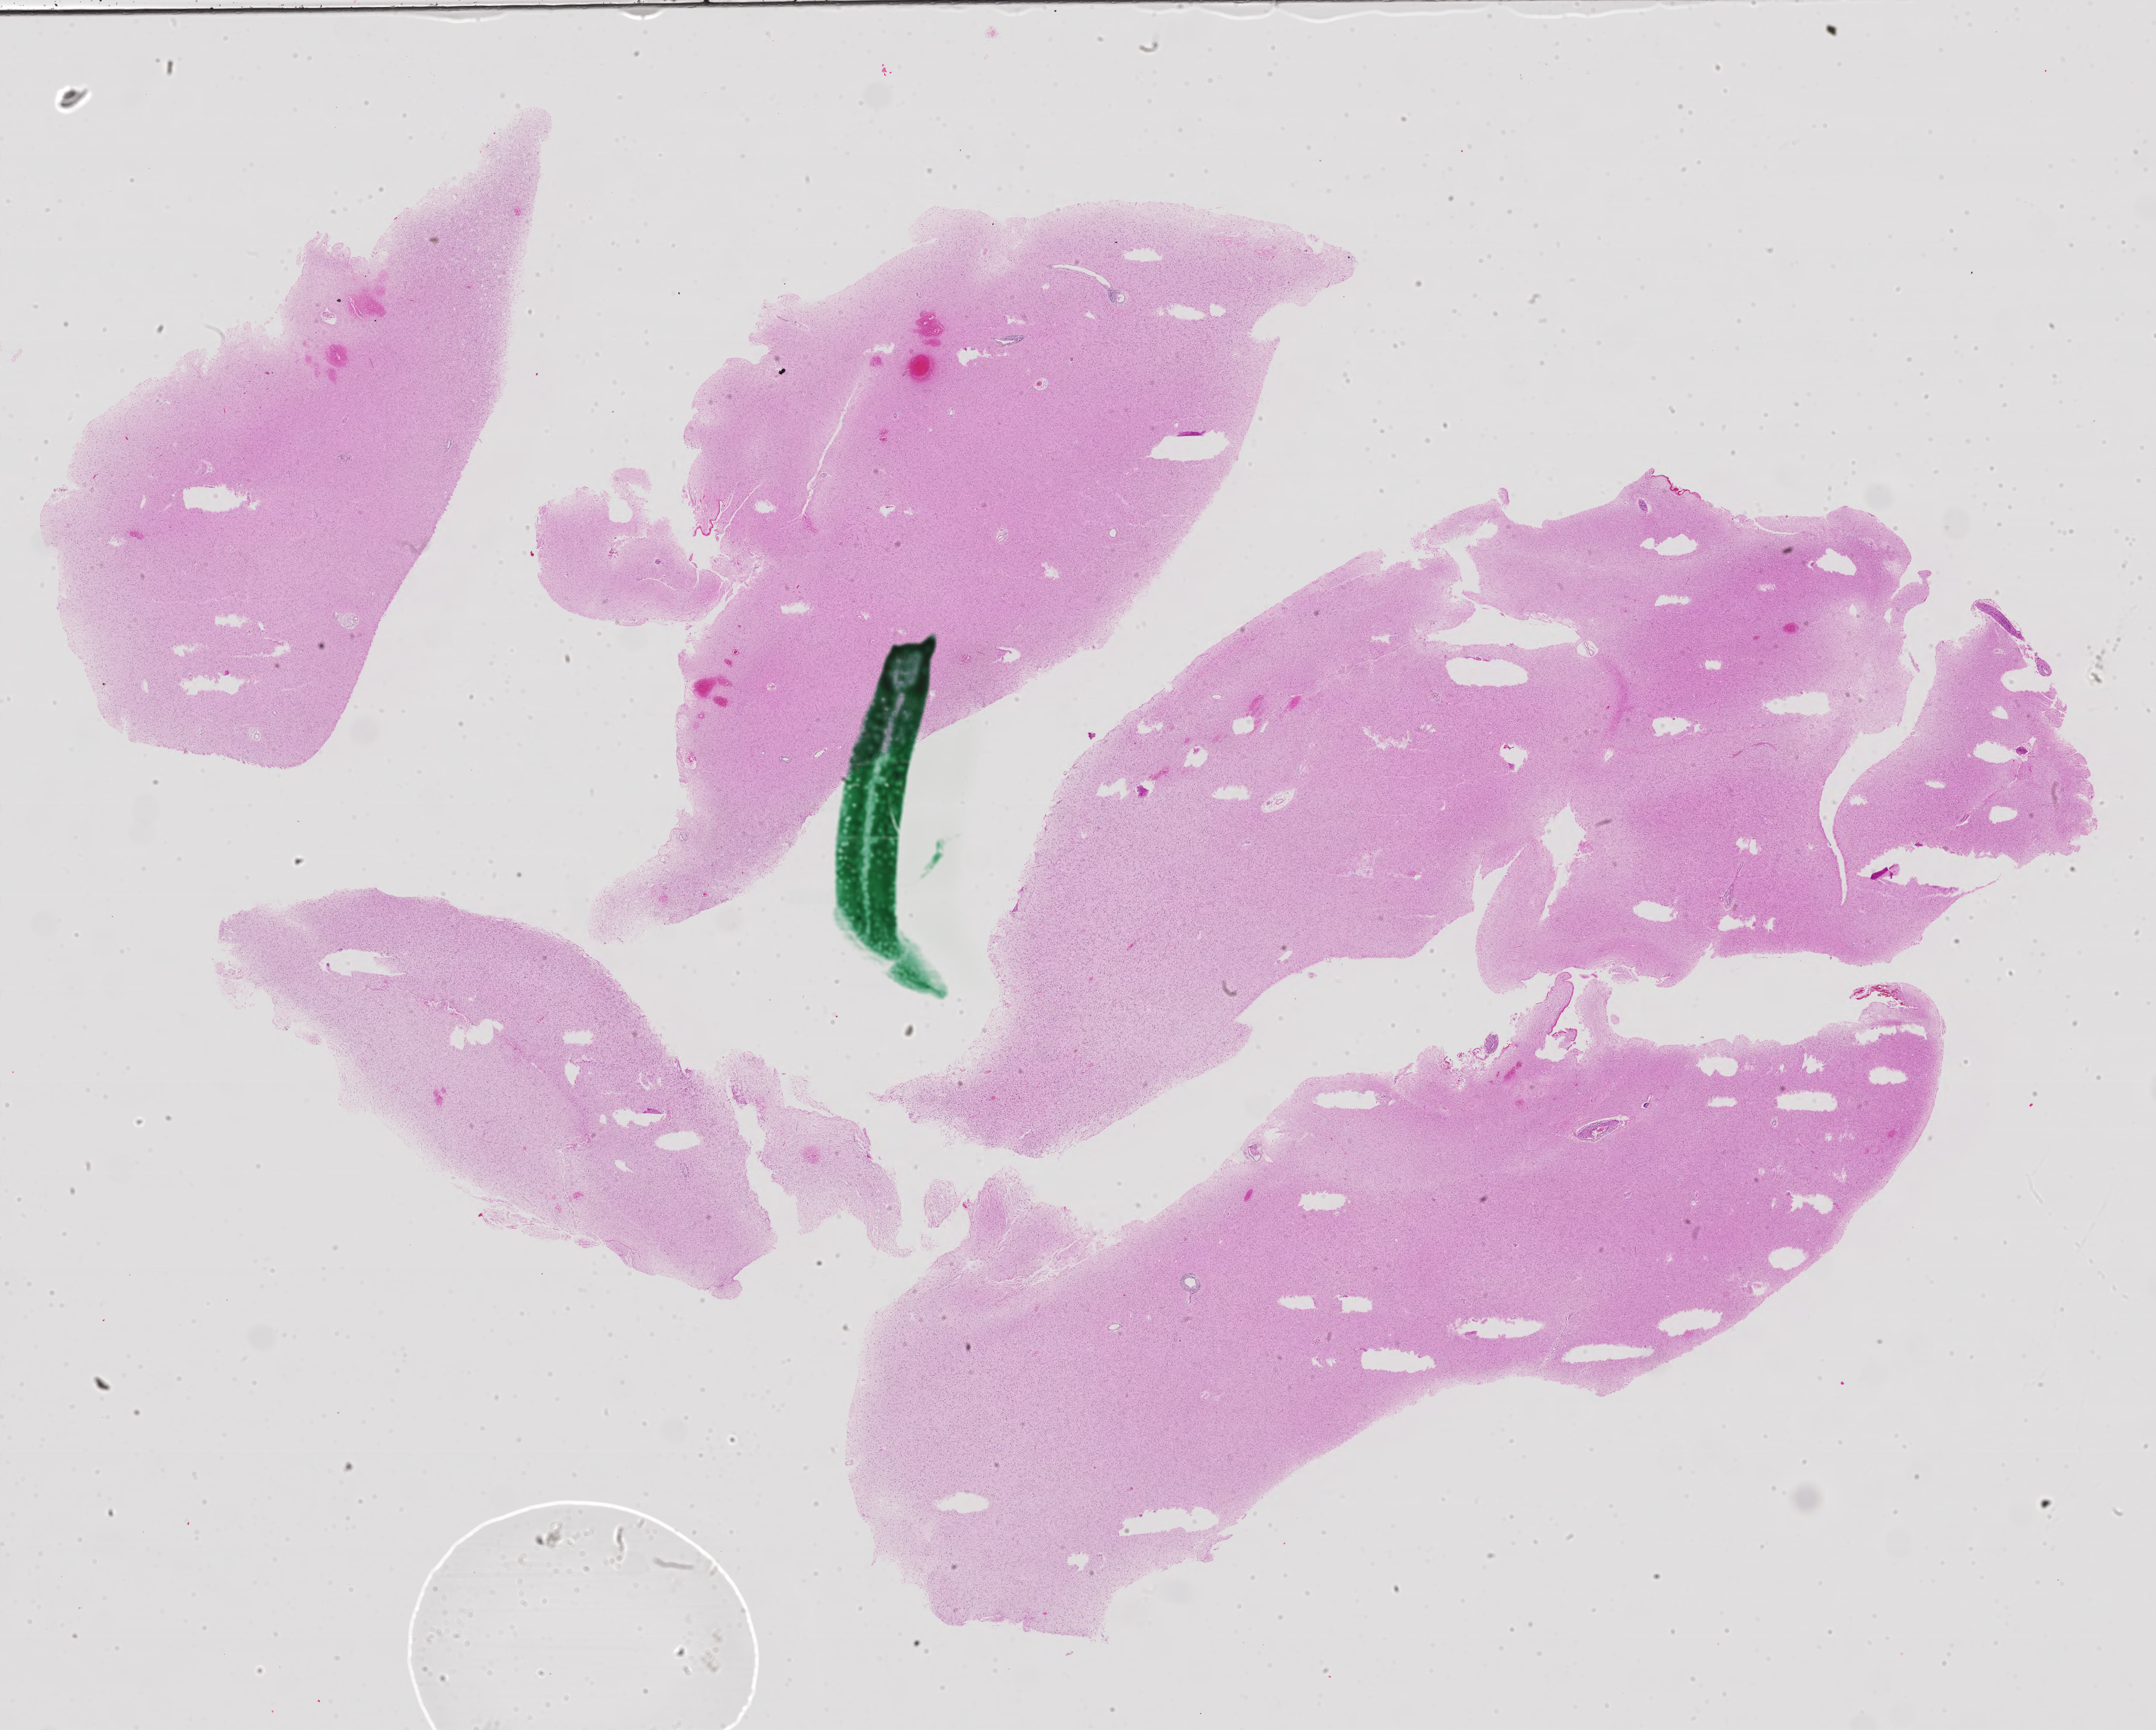
H&E-stained whole-slide image, low-resolution overview of the scanned area, about 29.3 x 23.5 mm, FFPE section, primary tumour sample from the brain. Male patient; age at initial diagnosis 28 years. Histologic grade: G2 (moderately differentiated).
Diagnosis: Mixed glioma (cerebrum).